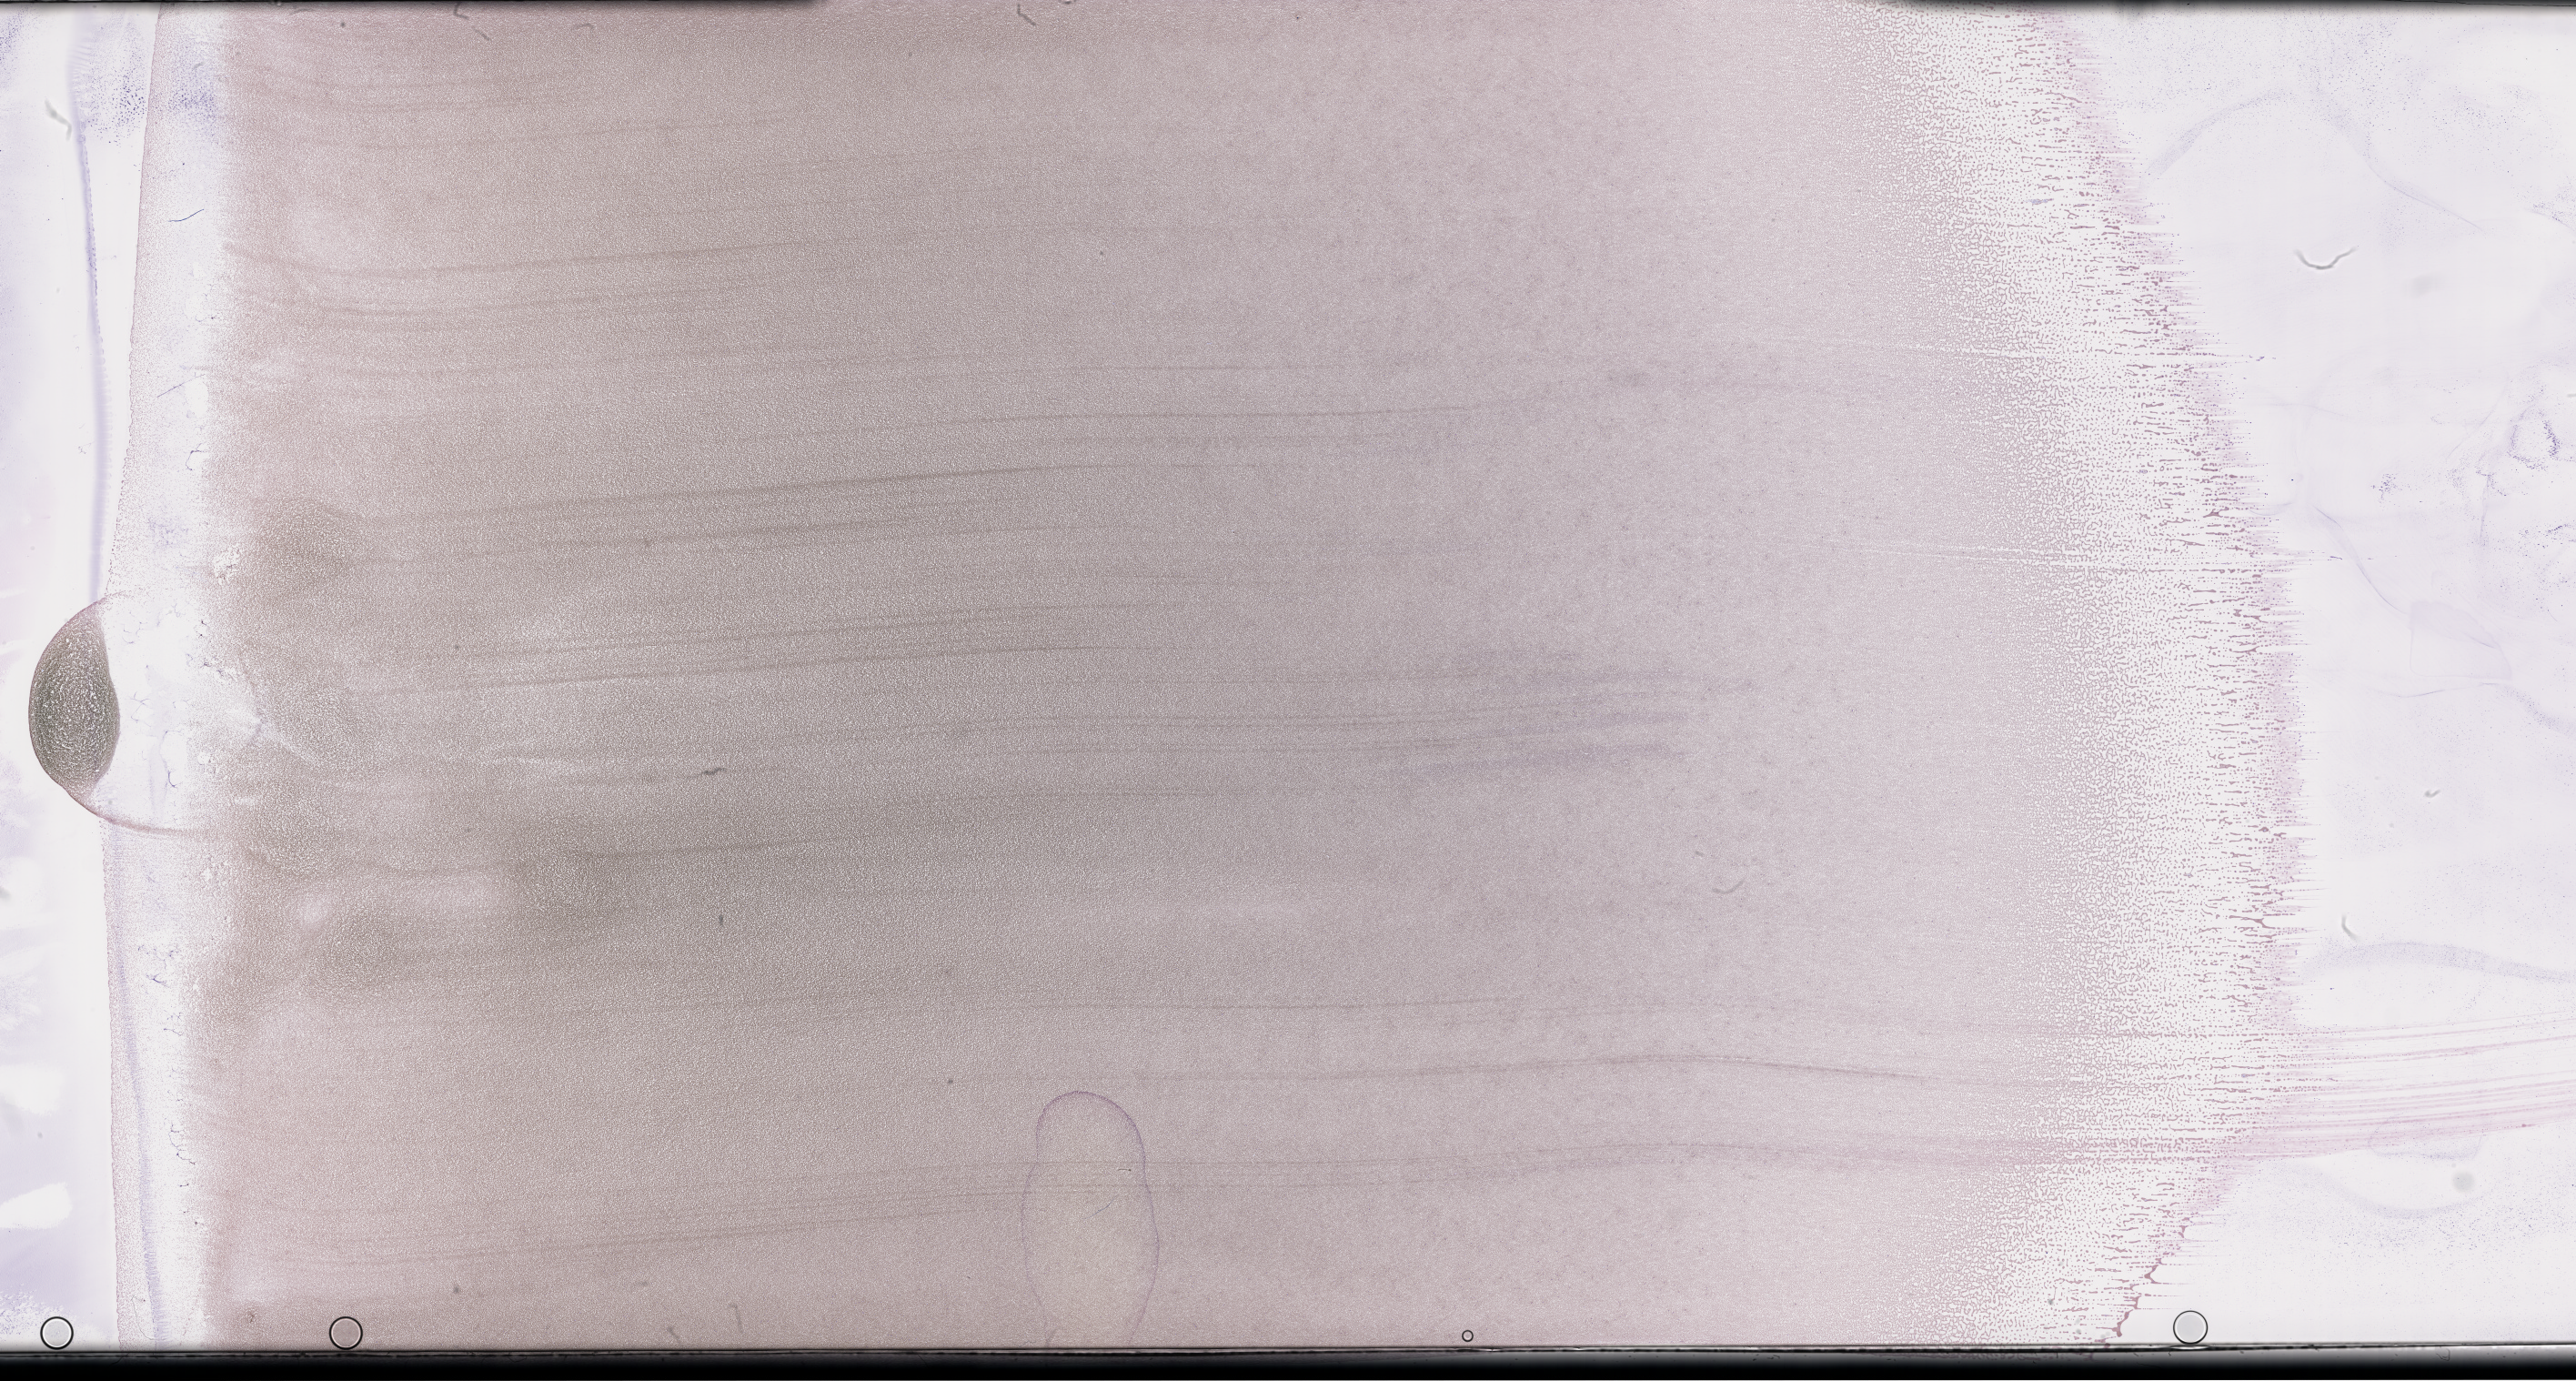
Wright-Giemsa-stained whole blood smear, whole-slide image — low-resolution overview of the scanned area, about 45.7 x 24.5 mm, EDTA-anticoagulated smear, collected on treatment. Patient: male.
From a patient with: Plasma Cell Myeloma.